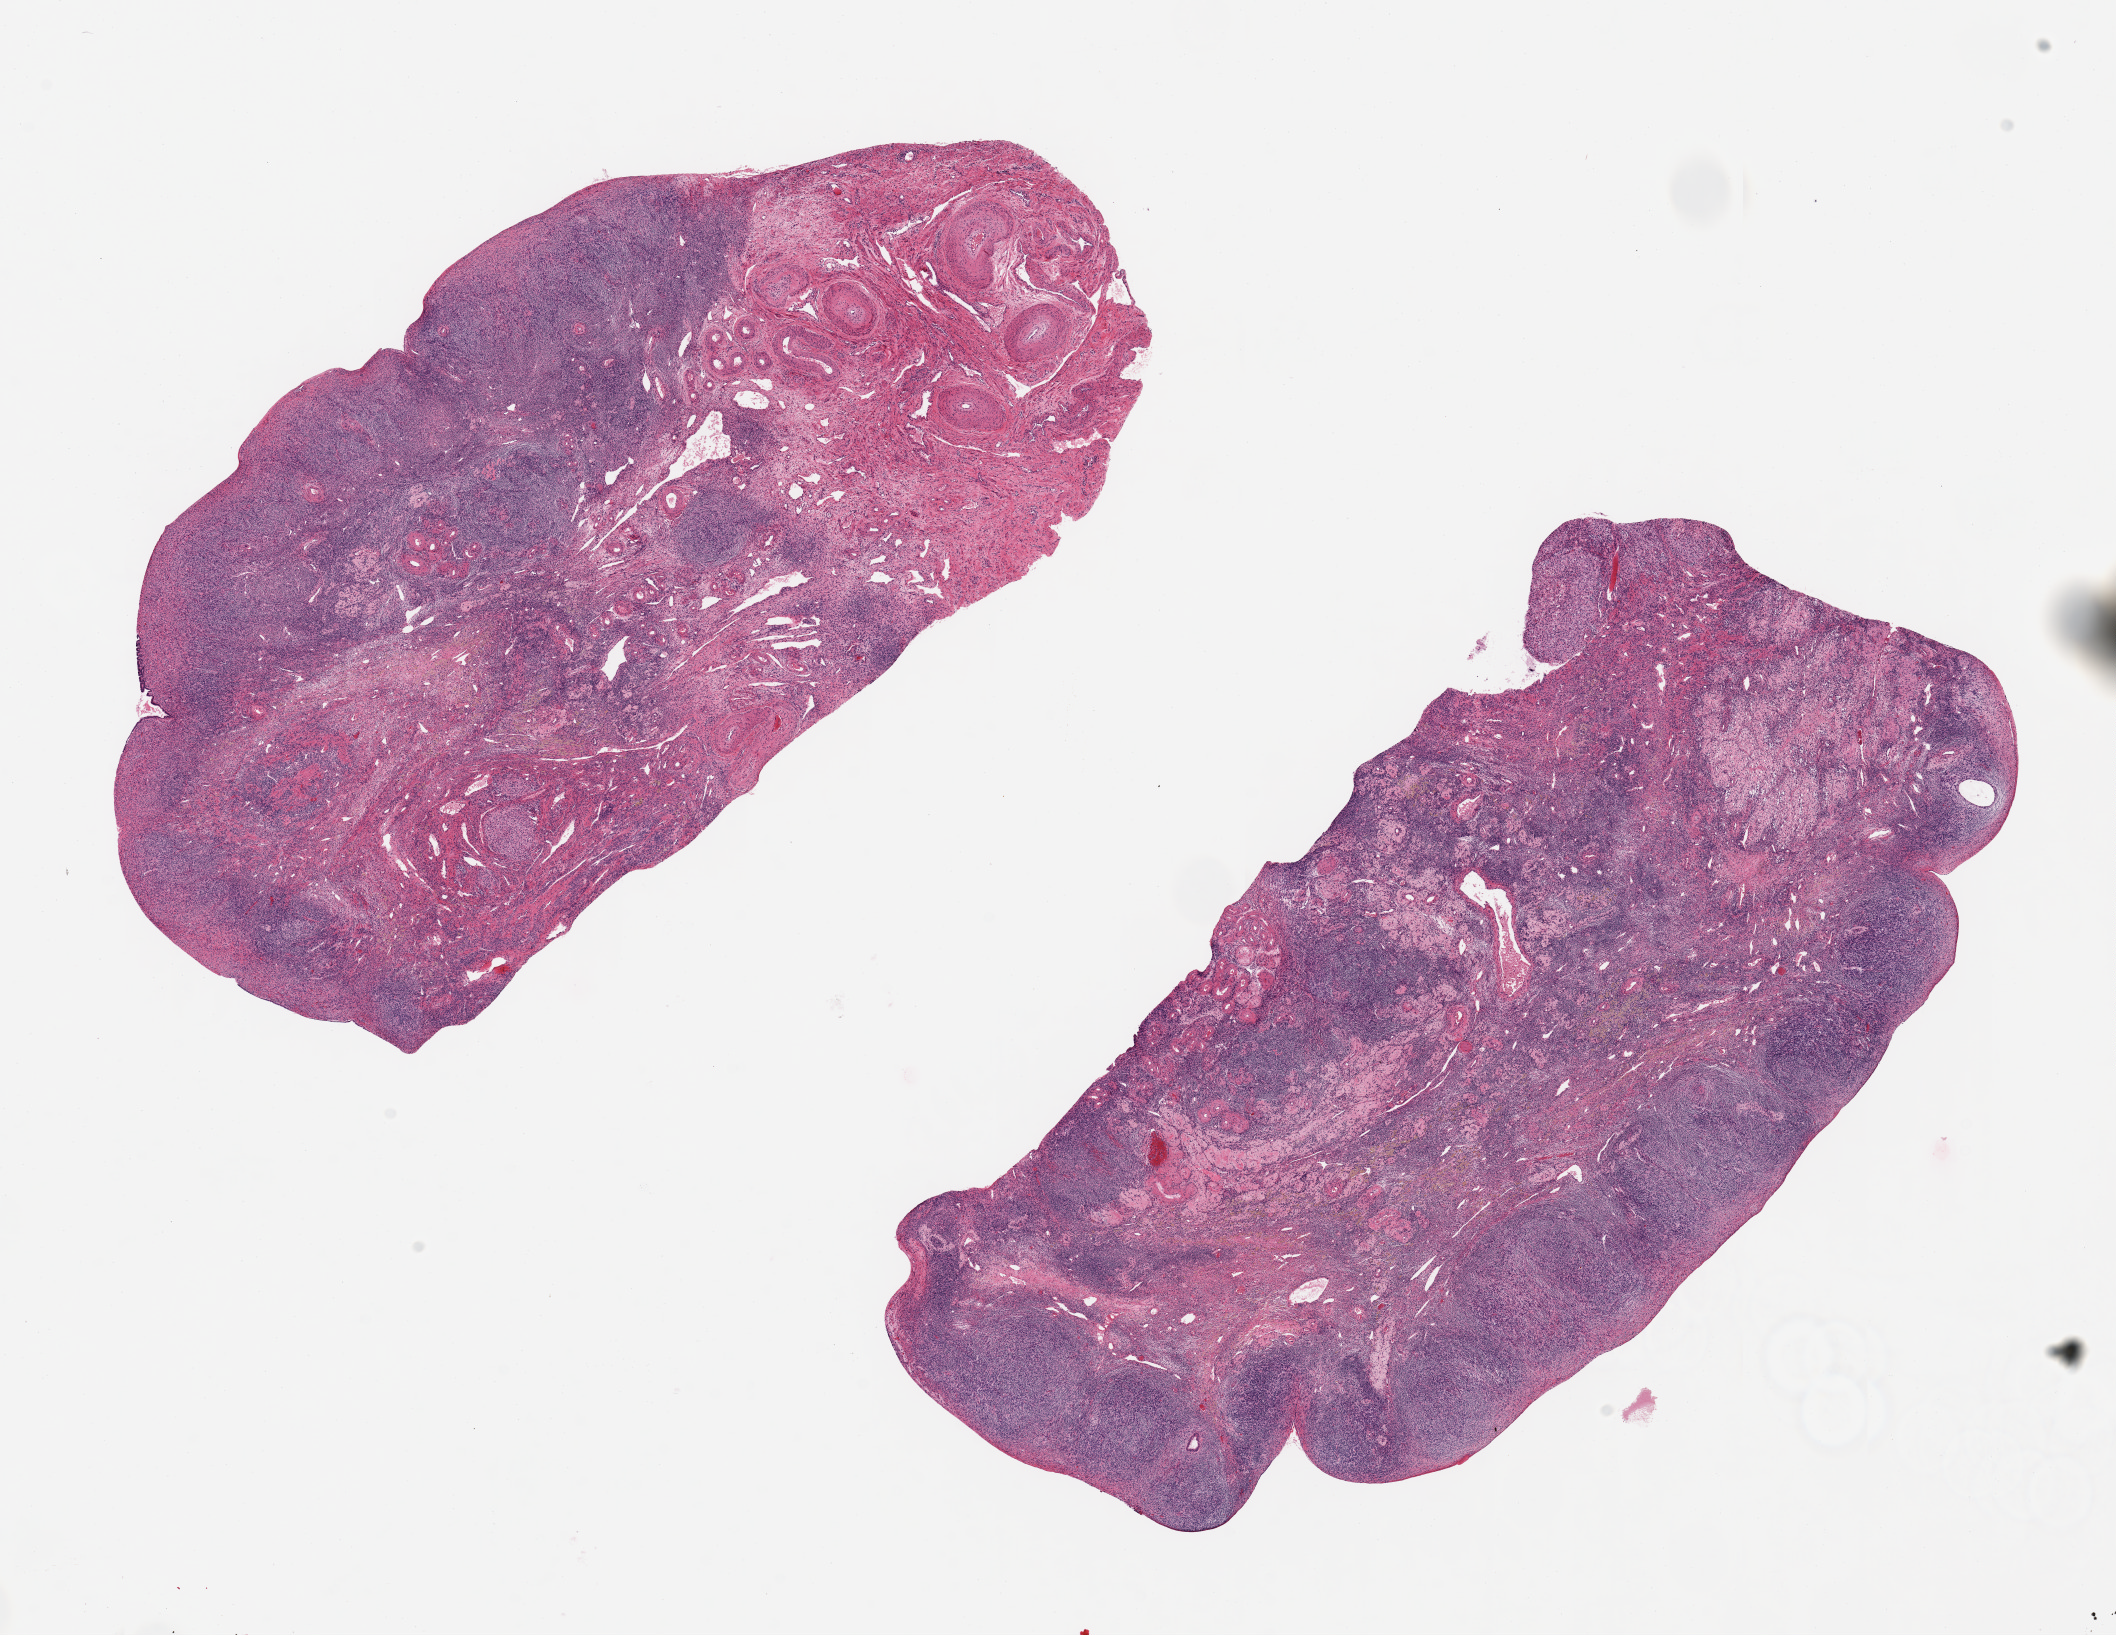
Whole-slide image, hematoxylin and eosin (H&E) stain — a low-resolution overview of the entire scanned area, about 16.7 x 12.9 mm (acquisition: 20x scan). PAXgene-fixed paraffin-embedded (PFPE) section. Sampled site (target tissue): ovary. Donor tissue sample. Donor sex: female.
Pathologist's review note for this sample: 2 ~9x5mm aliquots. No visible ova, involuted corpus luteum noted.